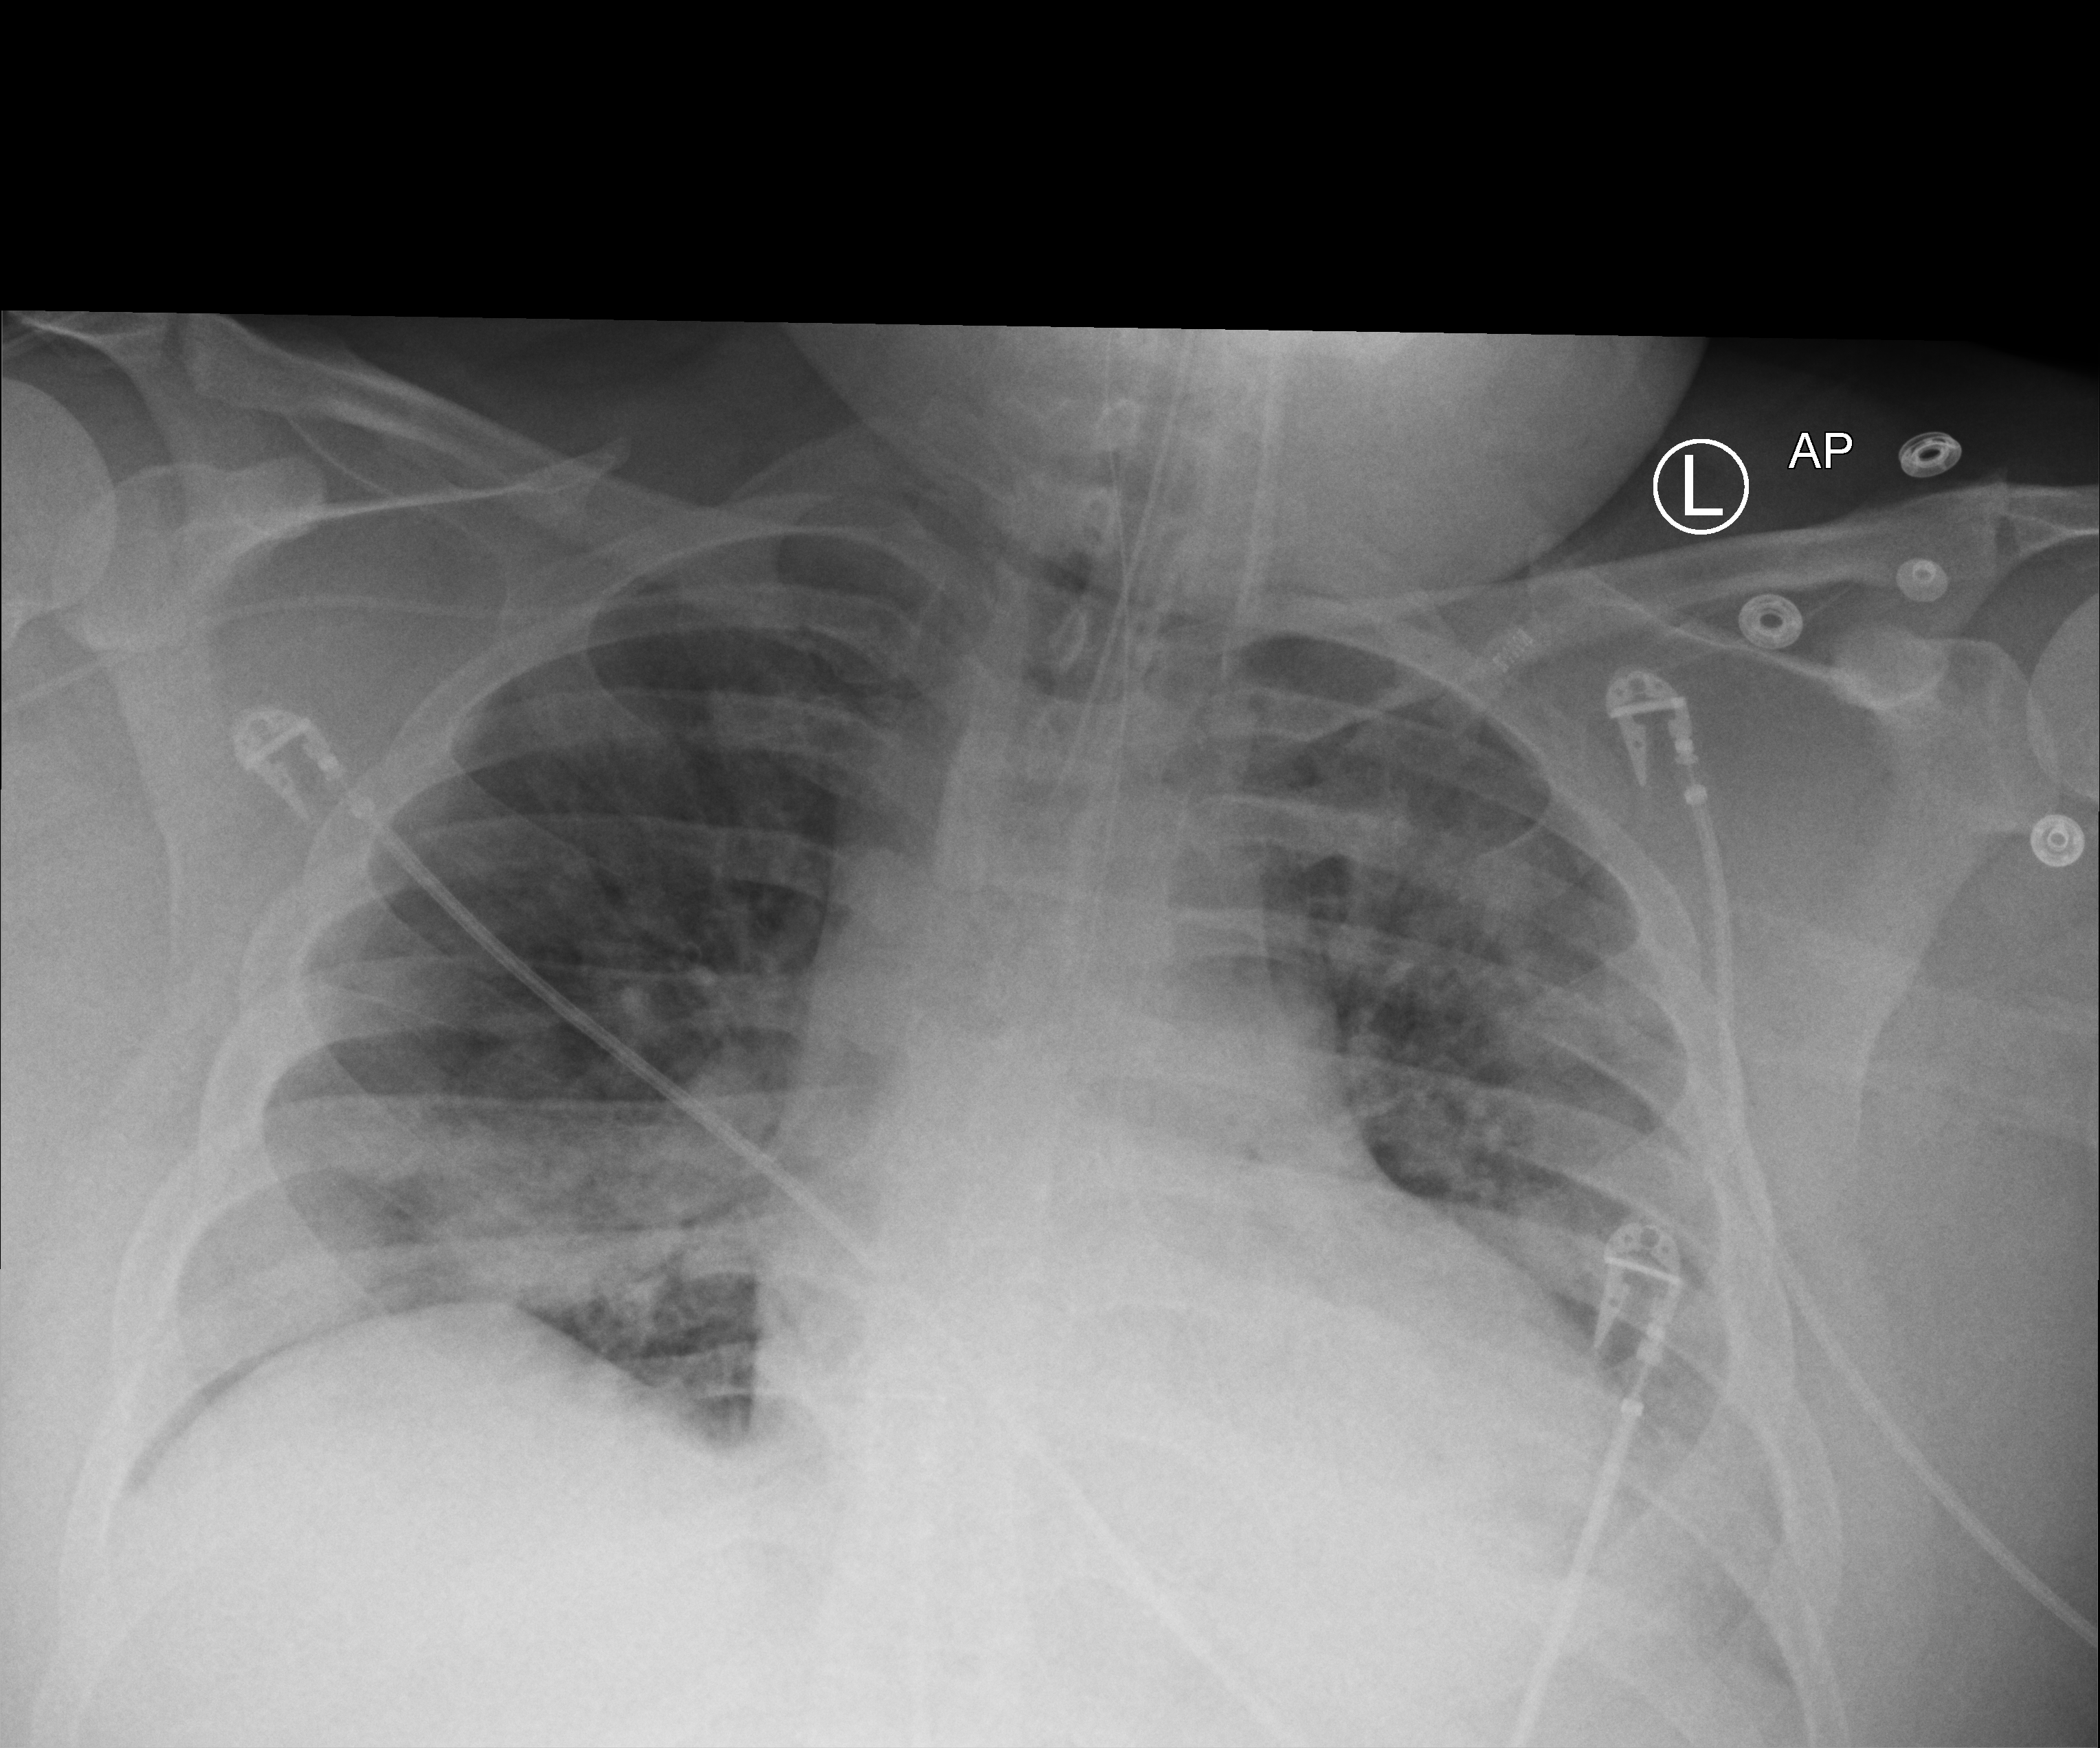
Portable chest radiograph; anteroposterior (AP) projection. Adult patient hospitalised with COVID-19, age 18–59 years.
From the hospital-stay record, not from the radiograph (when in the stay this image was taken is not recorded): length of hospital stay: 10 days; admitted to intensive care during this hospital stay: yes; mechanically ventilated during this hospital stay: yes.